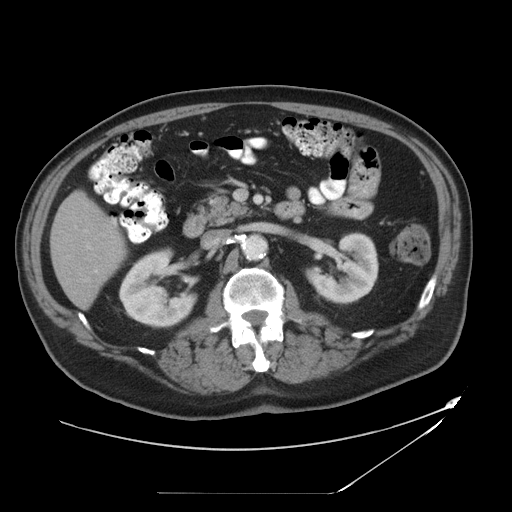
Contrast-enhanced abdominal CT, one axial slice. Position 18 of 49 along the scan axis. 120 kVp. Soft-tissue window (W 400 / L 40 HU). 512 × 512 image matrix. Male patient, age 72 years. From the clinical record (not read from this slice): diagnosis: colorectal cancer liver metastases, imaged before liver resection; multiple liver metastases: no; largest metastasis: 2.5 cm; disease in both lobes: no.
Annotated regions visible in this slice (expert manual segmentation):
- hepatic veins: box from (x=85, y=242) to (x=93, y=250) px
- liver: (x=52, y=193)–(x=124, y=306)
- planned liver remnant (the part of the liver to remain after resection): (x=52, y=194)–(x=124, y=306)